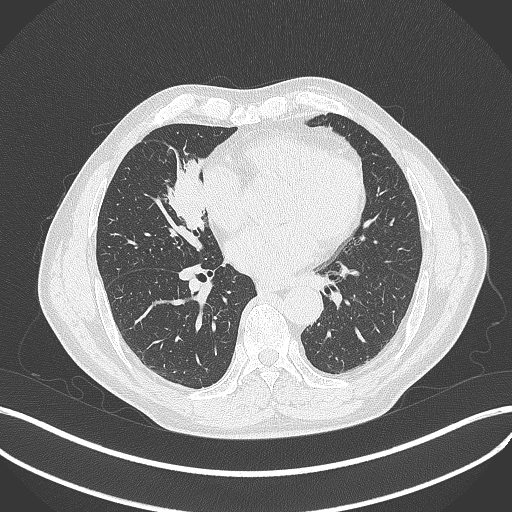
Chest CT, one axial slice; position 175 of 429 along the scan axis; reconstruction kernel B70f; lung window (W 1500 / L -600 HU); 1 mm slice thickness; 512 × 512 image matrix. Male patient, age 61 years. From the clinical record (not read from this slice): clinical TNM (as recorded): T2b N1 M0.
Structures marked on this image (rectangle marked by the reading radiologist):
- lung tumour (recorded histology: squamous cell carcinoma): box from (x=160, y=153) to (x=212, y=236) px